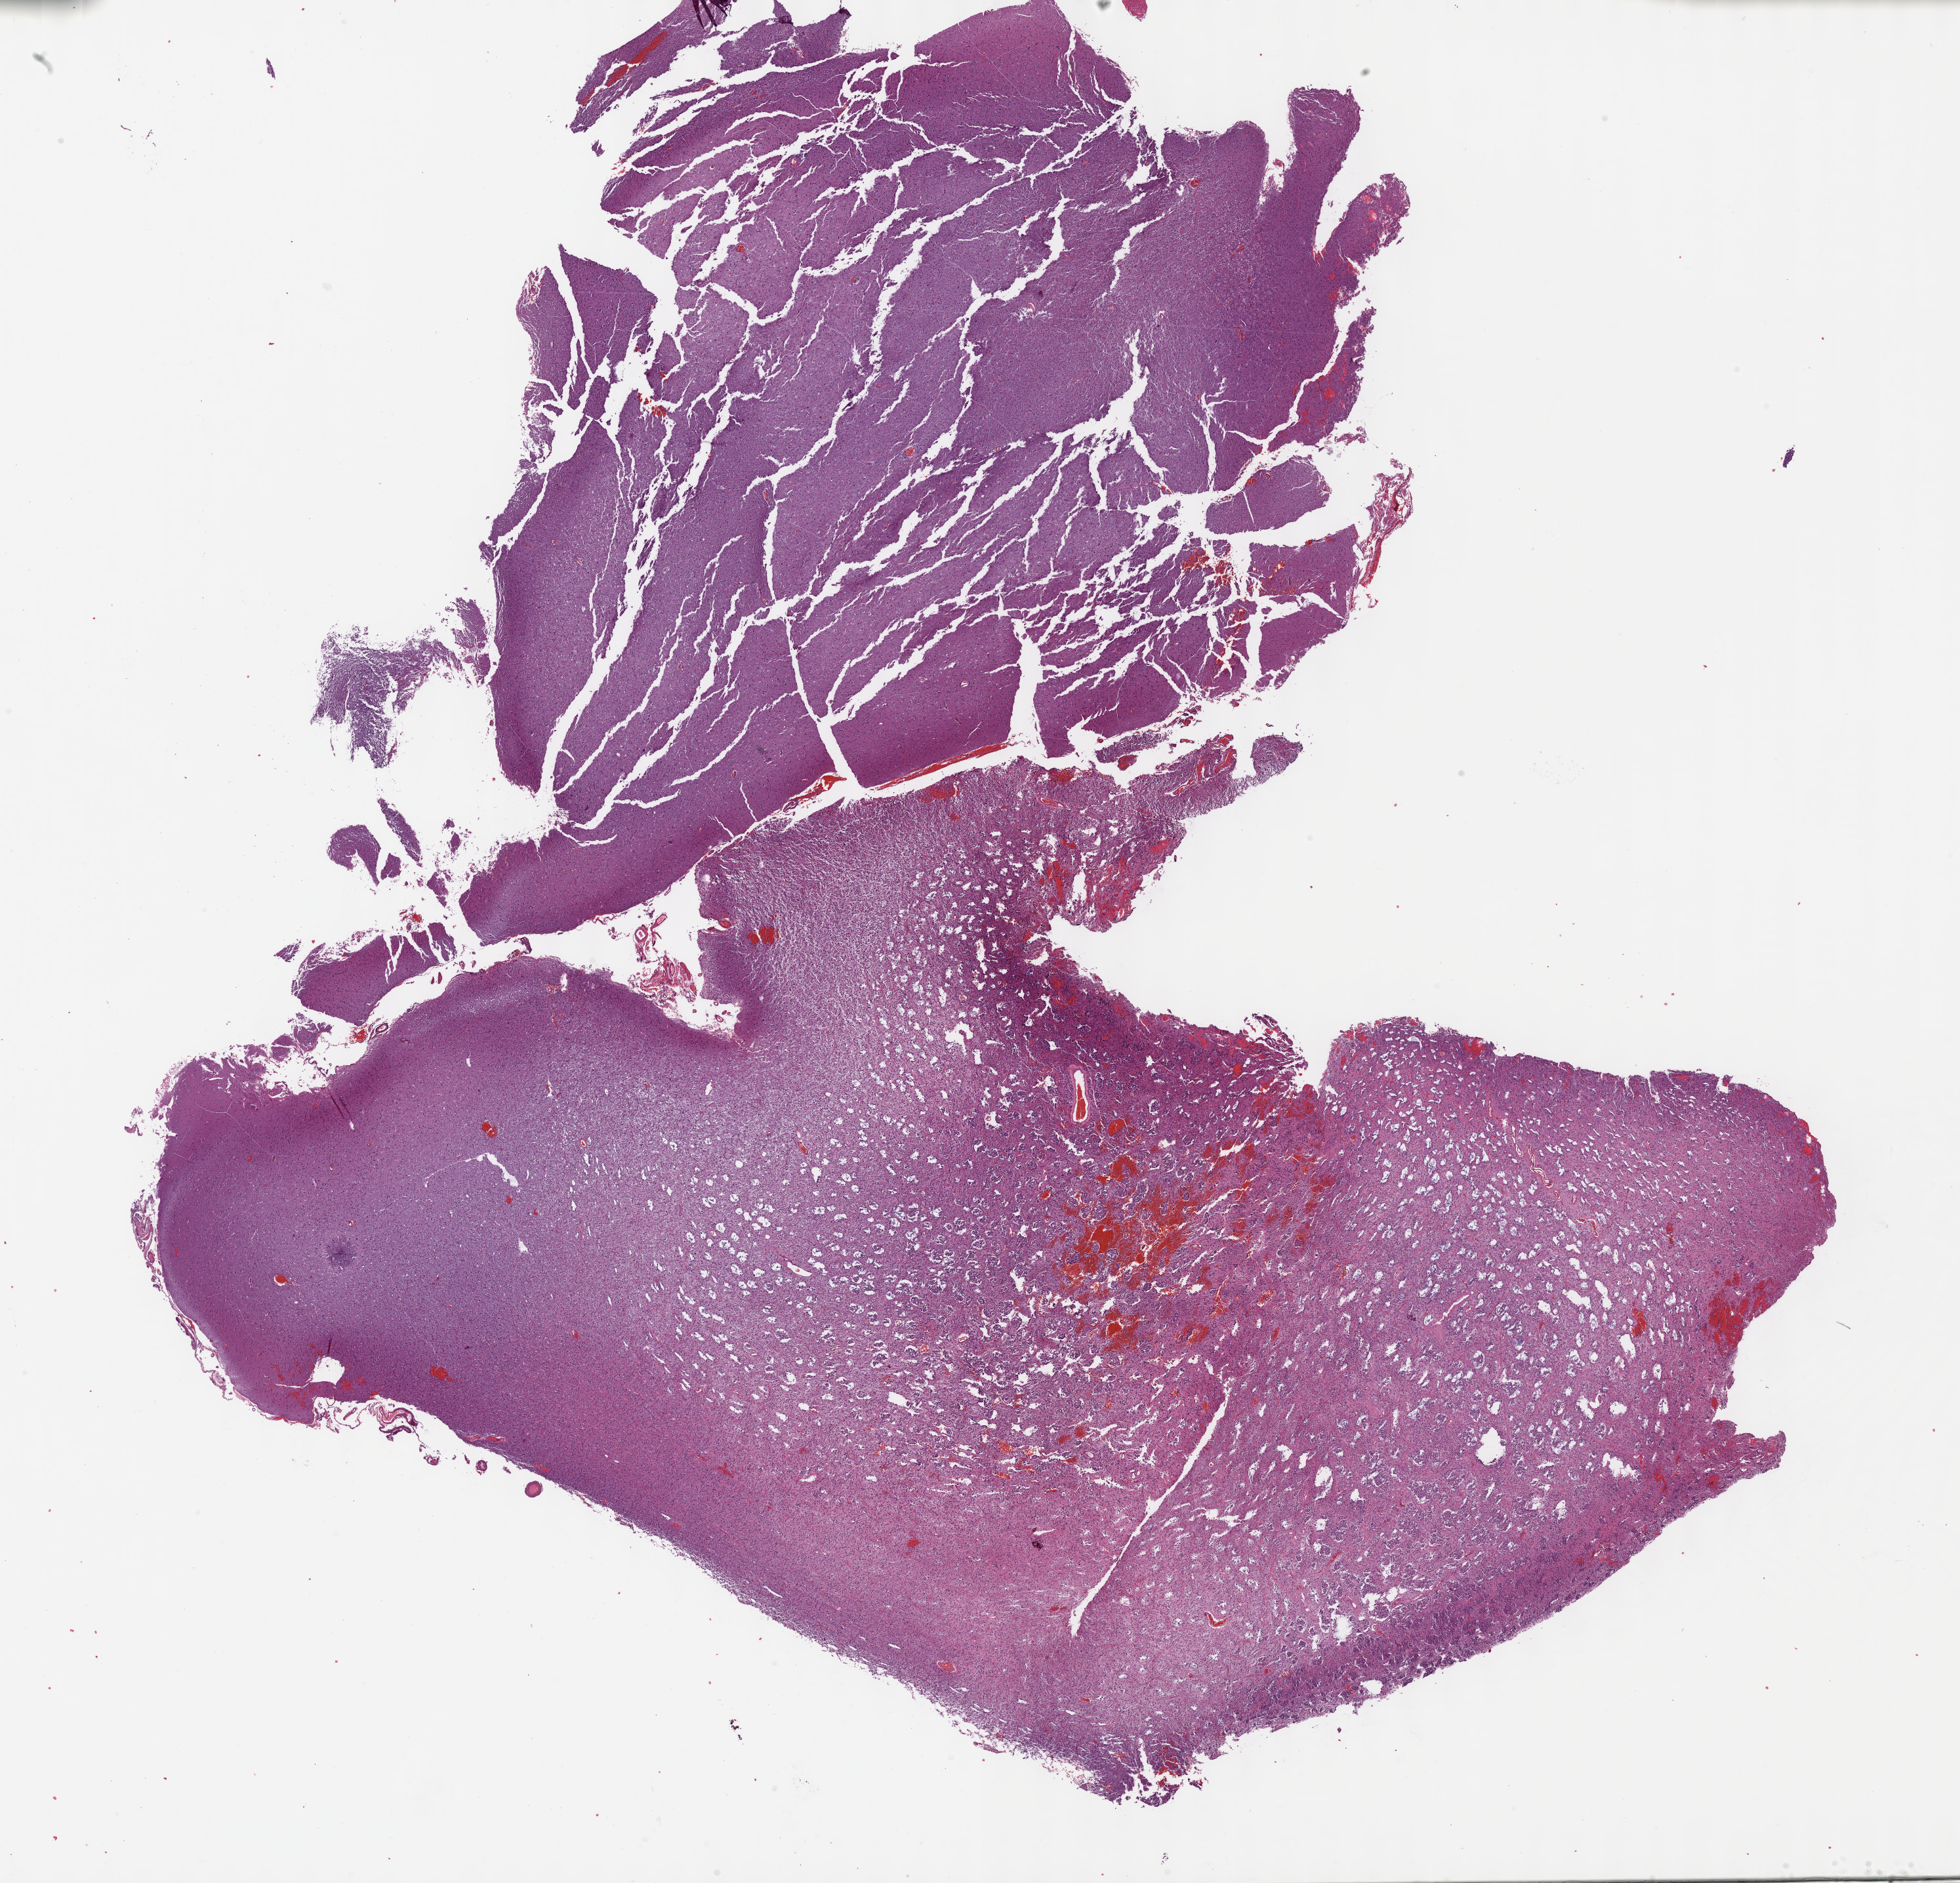
H&E whole-slide image, a low-resolution overview of the entire scanned area, about 24.1 x 23.2 mm (from a 40x scan); formalin-fixed paraffin-embedded (FFPE) diagnostic section; brain, primary tumour sample. Male, age 28 years at initial diagnosis. Histologic grade: G2 (moderately differentiated).
Histologic diagnosis: Astrocytoma, NOS (cerebrum).